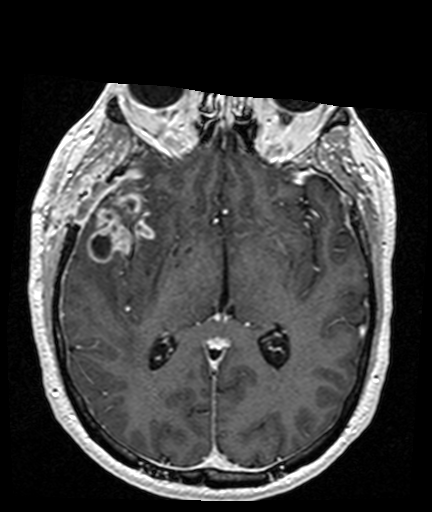
Brain MRI from a brain-tumour surgery series, one axial slice. Position 90 of 176 along the scan axis. T1-weighted post-contrast. 432 × 512 image matrix, field of view 194 × 230 mm. From the clinical record (not read from this slice): histopathology: Glioblastoma; WHO grade: 4; IDH mutation: no.
Annotated regions visible in this slice (expert manual segmentation):
- tumour: bounding box [x1, y1, x2, y2] px = [87, 188, 154, 264]